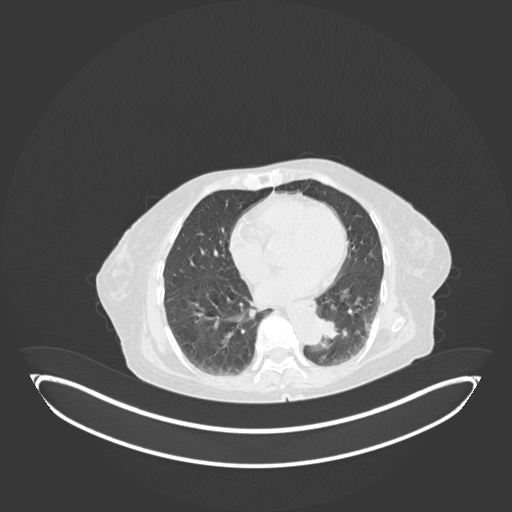
Chest CT, one axial slice. Position 34 of 189 along the scan axis. Reconstruction kernel B30f. Lung window (W 1500 / L -600 HU). 512 × 512 image matrix, field of view 500 × 500 mm. Female patient, age 82 years. Case-level facts recorded for this patient, not image findings: clinical TNM (as recorded): T1b N0 M1.
Outlined on this slice (bounding box drawn by a radiologist):
- lung tumour (recorded histology: adenocarcinoma): bounding box [x1, y1, x2, y2] px = [316, 311, 343, 348]